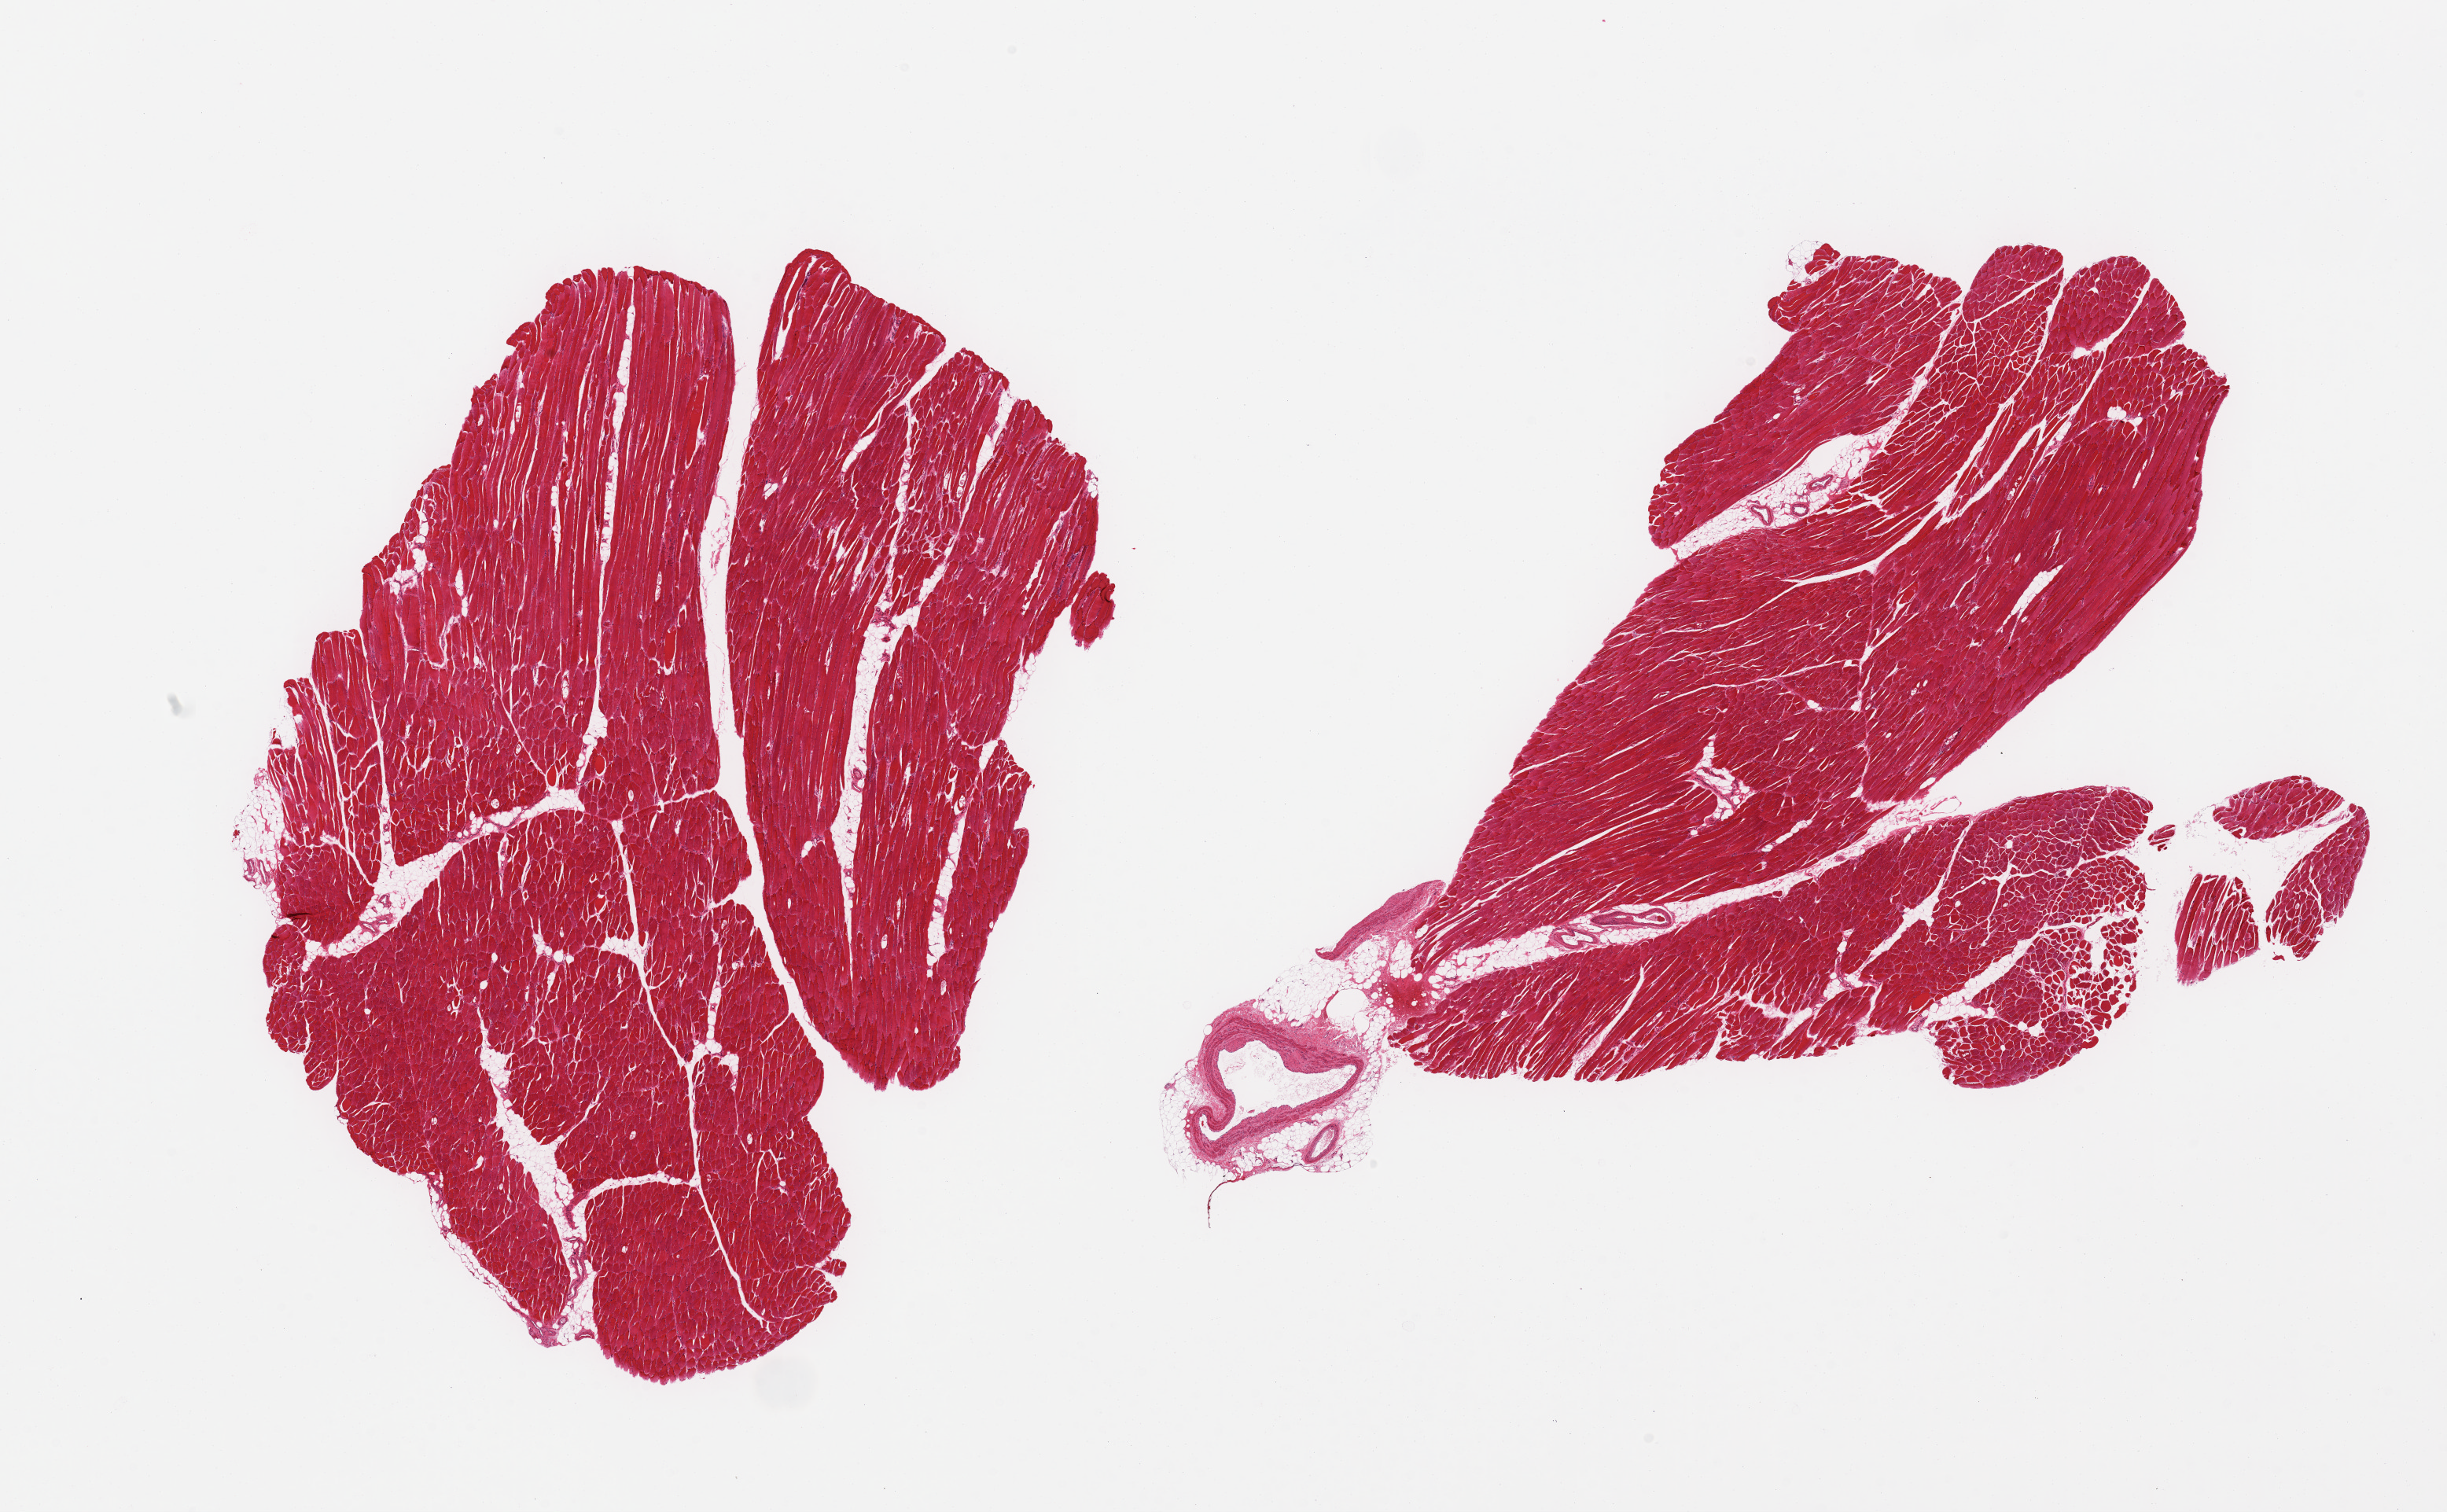
Digitized H&E-stained section, brightfield — shown as a low-resolution overview of the whole scanned area (about 24.6 x 15.2 mm). PAXgene-fixed, paraffin-embedded tissue. Sampled site (target tissue): skeletal muscle. Tissue donor sample.
Review note (as recorded): 2 pieces; fat content <5%.